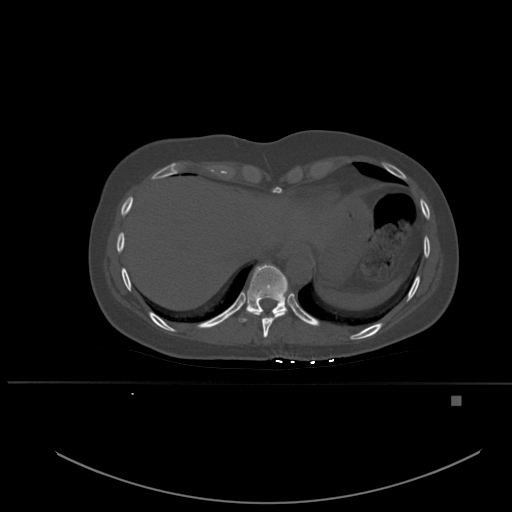
CT including the spine, one axial slice. Bone window (W 1800 / L 400 HU). 1.5 mm slice thickness. 512 × 512 image matrix, field of view 443 × 443 mm. Female patient, age 49 years. Case-level facts recorded for this patient, not image findings: primary cancer: breast.
Annotated regions visible in this slice (semi-automatic segmentation, software-assisted and operator-edited):
- T10 vertebra: bounding box <239,264,288,322> (left, top, right, bottom; pixels)
- T9 vertebra: <246,308,287,338>